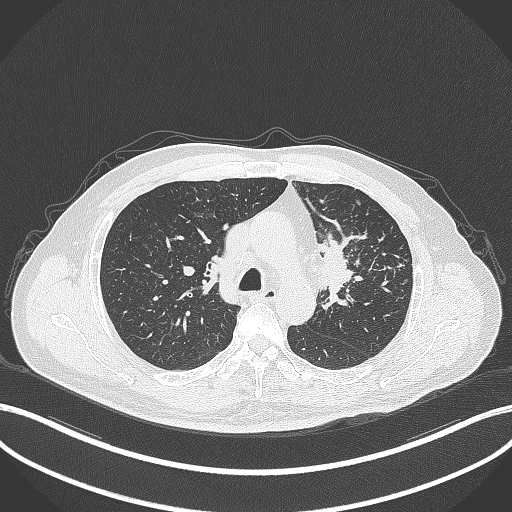
Chest CT, one axial slice; slice 240 of 386 in the series (ordered by position); reconstruction kernel B70f; 120 kVp; lung window (W 1500 / L -600 HU); 1 mm slice thickness; 512 × 512 image matrix. Male patient, age 69 years. From the clinical record (not read from this slice): clinical TNM (as recorded): T2a N2 M0.
Outlined on this slice (rectangle marked by the reading radiologist):
- lung tumour (recorded histology: adenocarcinoma): bounding box <319,231,358,309> (left, top, right, bottom; pixels)